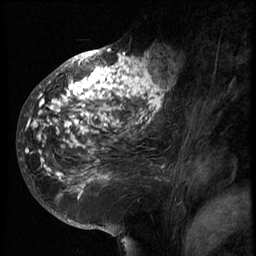
Breast MRI (dynamic contrast-enhanced), one sagittal slice. Slice 35 of 66 in the series (ordered by position). 3 images stored at this slice position (order not interpretable as contrast timing). 1.5 T. TE 4.2 ms, TR 8.9 ms. 2.5 mm slice thickness. 256 × 256 image matrix, field of view 200 × 200 mm. Patient: female, 39 years. From the clinical record (not read from this slice): setting: breast cancer imaged before/during neoadjuvant chemotherapy; receptor status: HER2-positive.
Outlined on this slice (semi-automatically segmented with operator editing):
- analysis volume of interest (the breast-tissue region the enhancement analysis was run in; not a lesion): bounding box <29,44,166,196> (left, top, right, bottom; pixels)
- tumour enhancement mask (voxels above the 140 % enhancement threshold inside the analysis volume of interest): <29,48,166,181>